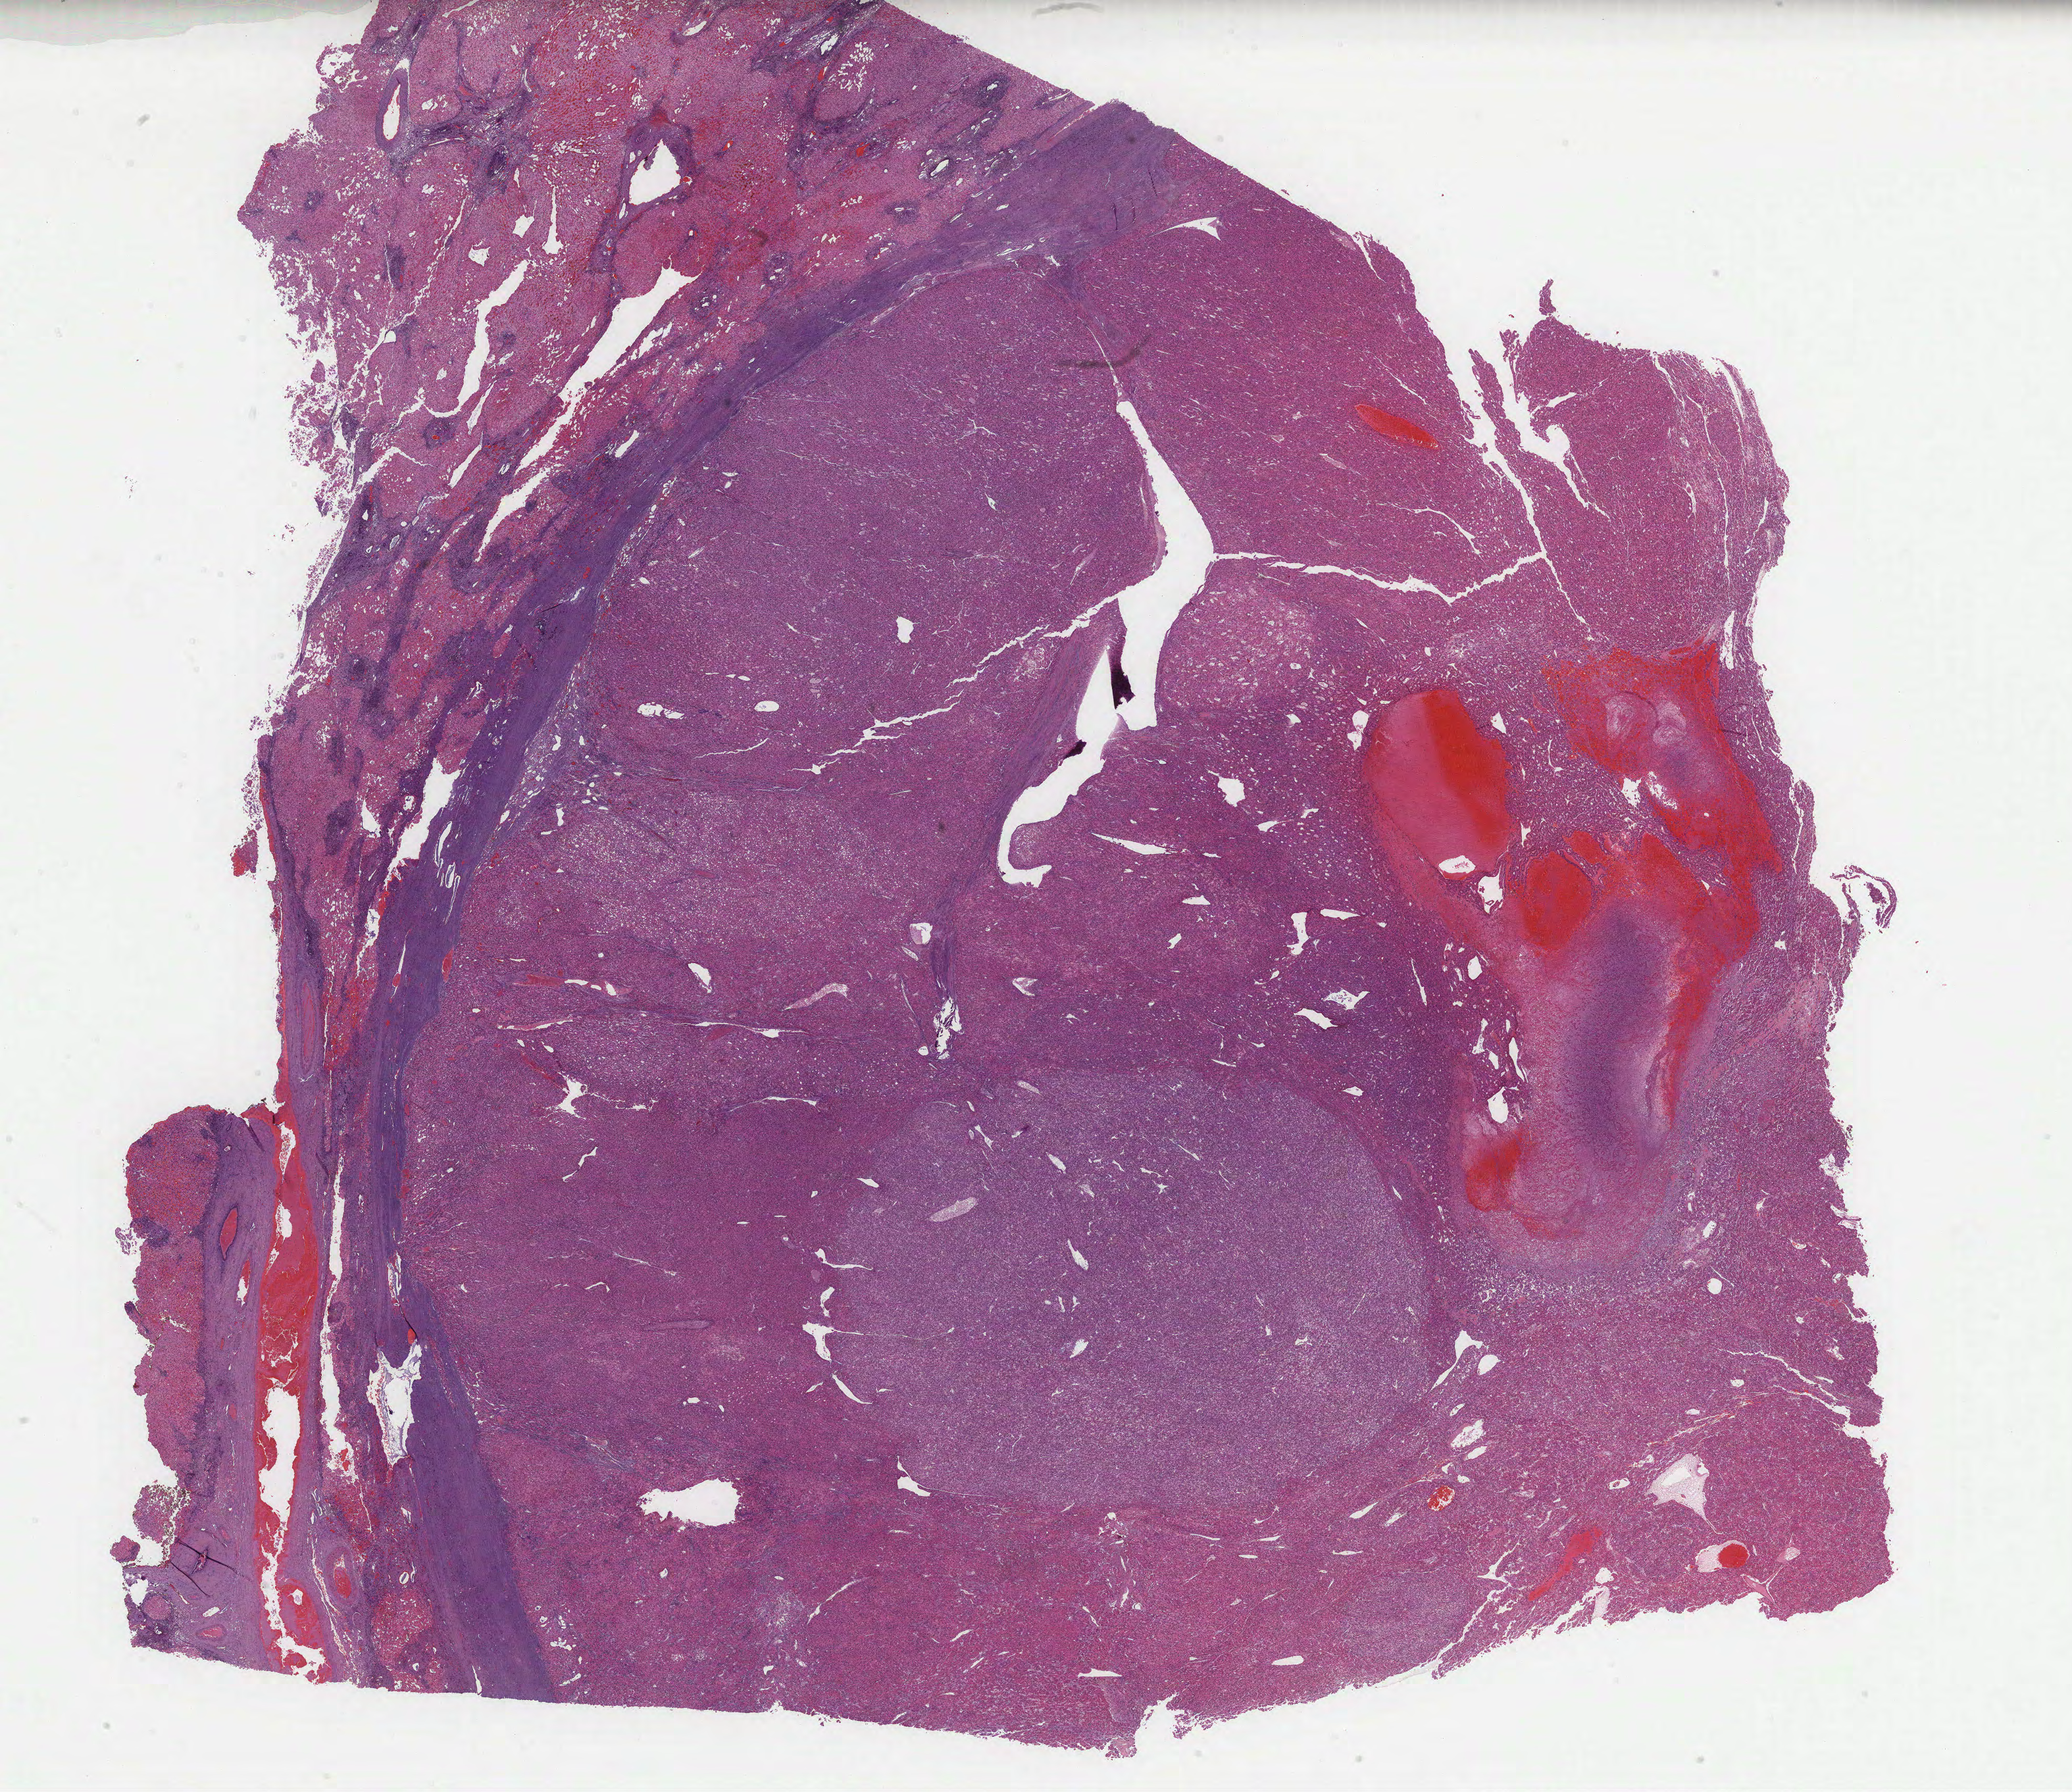
Hematoxylin and eosin (H&E) stained whole-slide image, shown as a low-resolution overview of the whole scanned area (about 25.4 x 22.0 mm); formalin-fixed paraffin-embedded (FFPE) diagnostic section; primary tumour sample from the liver. Patient: male, age at initial diagnosis 70 years. Histologic grade: G2 (moderately differentiated).
Diagnosis: Hepatocellular carcinoma, NOS. AJCC pathologic stage: I.